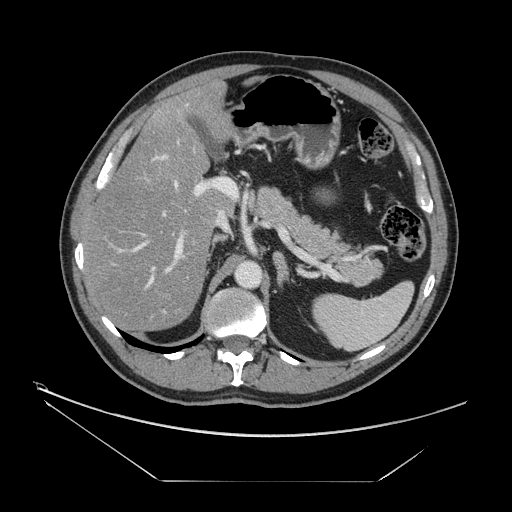
Contrast-enhanced abdominal CT, one axial slice; position 89 of 161 along the scan axis; reconstruction kernel STANDARD; intravenous contrast given; soft-tissue window (W 400 / L 40 HU); 2.5 mm slice thickness; 512 × 512 image matrix, field of view 440 × 440 mm. Male patient, age 65 years. From the clinical record (not read from this slice): diagnosis: colorectal cancer liver metastases, imaged before liver resection; multiple liver metastases: yes; largest metastasis: 4.2 cm.
Annotated regions visible in this slice (outlined manually by an expert reader):
- hepatic veins: box from (x=112, y=176) to (x=178, y=289) px
- liver: (x=85, y=85)–(x=231, y=330)
- planned liver remnant (the part of the liver to remain after resection): (x=85, y=85)–(x=231, y=329)
- portal vein (with intrahepatic branches): (x=111, y=154)–(x=236, y=320)